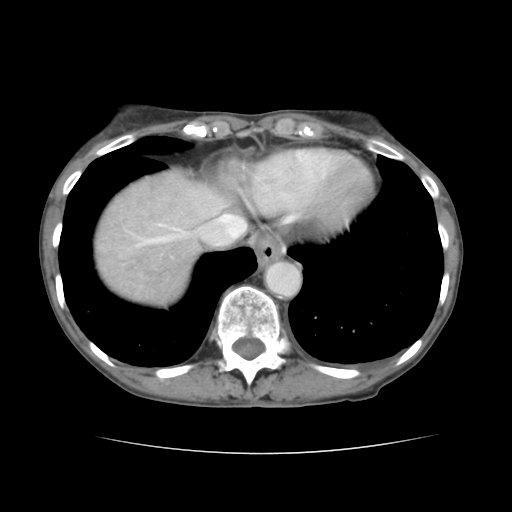
Contrast-enhanced abdominal CT, one axial slice. Position 127 of 136 along the scan axis. Intravenous contrast given. Soft-tissue window (W 400 / L 40 HU). 2.5 mm slice thickness. 512 × 512 image matrix, field of view 319 × 319 mm. Female patient, age 77 years. From the clinical record (not read from this slice): diagnosis: colorectal cancer liver metastases, imaged before liver resection; multiple liver metastases: yes; largest metastasis: 3 cm; chemotherapy before resection: yes.
Annotated regions visible in this slice (expert manual segmentation):
- hepatic veins: bounding box [x1, y1, x2, y2] px = [133, 196, 246, 248]
- liver: [95, 171, 227, 305]
- planned liver remnant (the part of the liver to remain after resection): [197, 184, 226, 215]